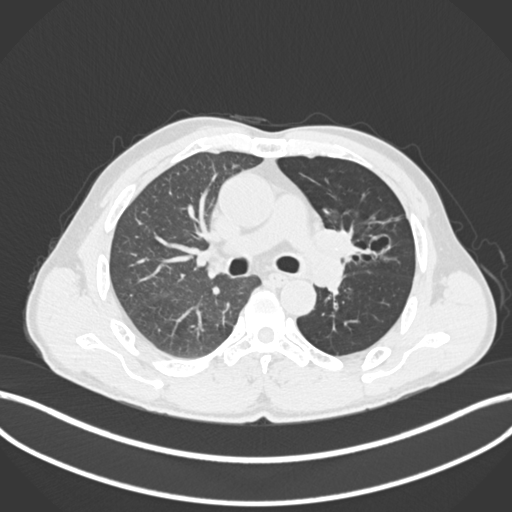
Chest CT, one axial slice. Position 116 of 255 along the scan axis. 120 kVp. Lung window (W 1500 / L -600 HU). 1 mm slice thickness. 512 × 512 image matrix, field of view 400 × 400 mm. Male patient, age 57 years. From the clinical record (not read from this slice): clinical TNM (as recorded): T2b N0 M0.
Outlined on this slice (rectangle marked by the reading radiologist):
- lung tumour (recorded histology: squamous cell carcinoma): bounding box <310,218,378,267> (left, top, right, bottom; pixels)